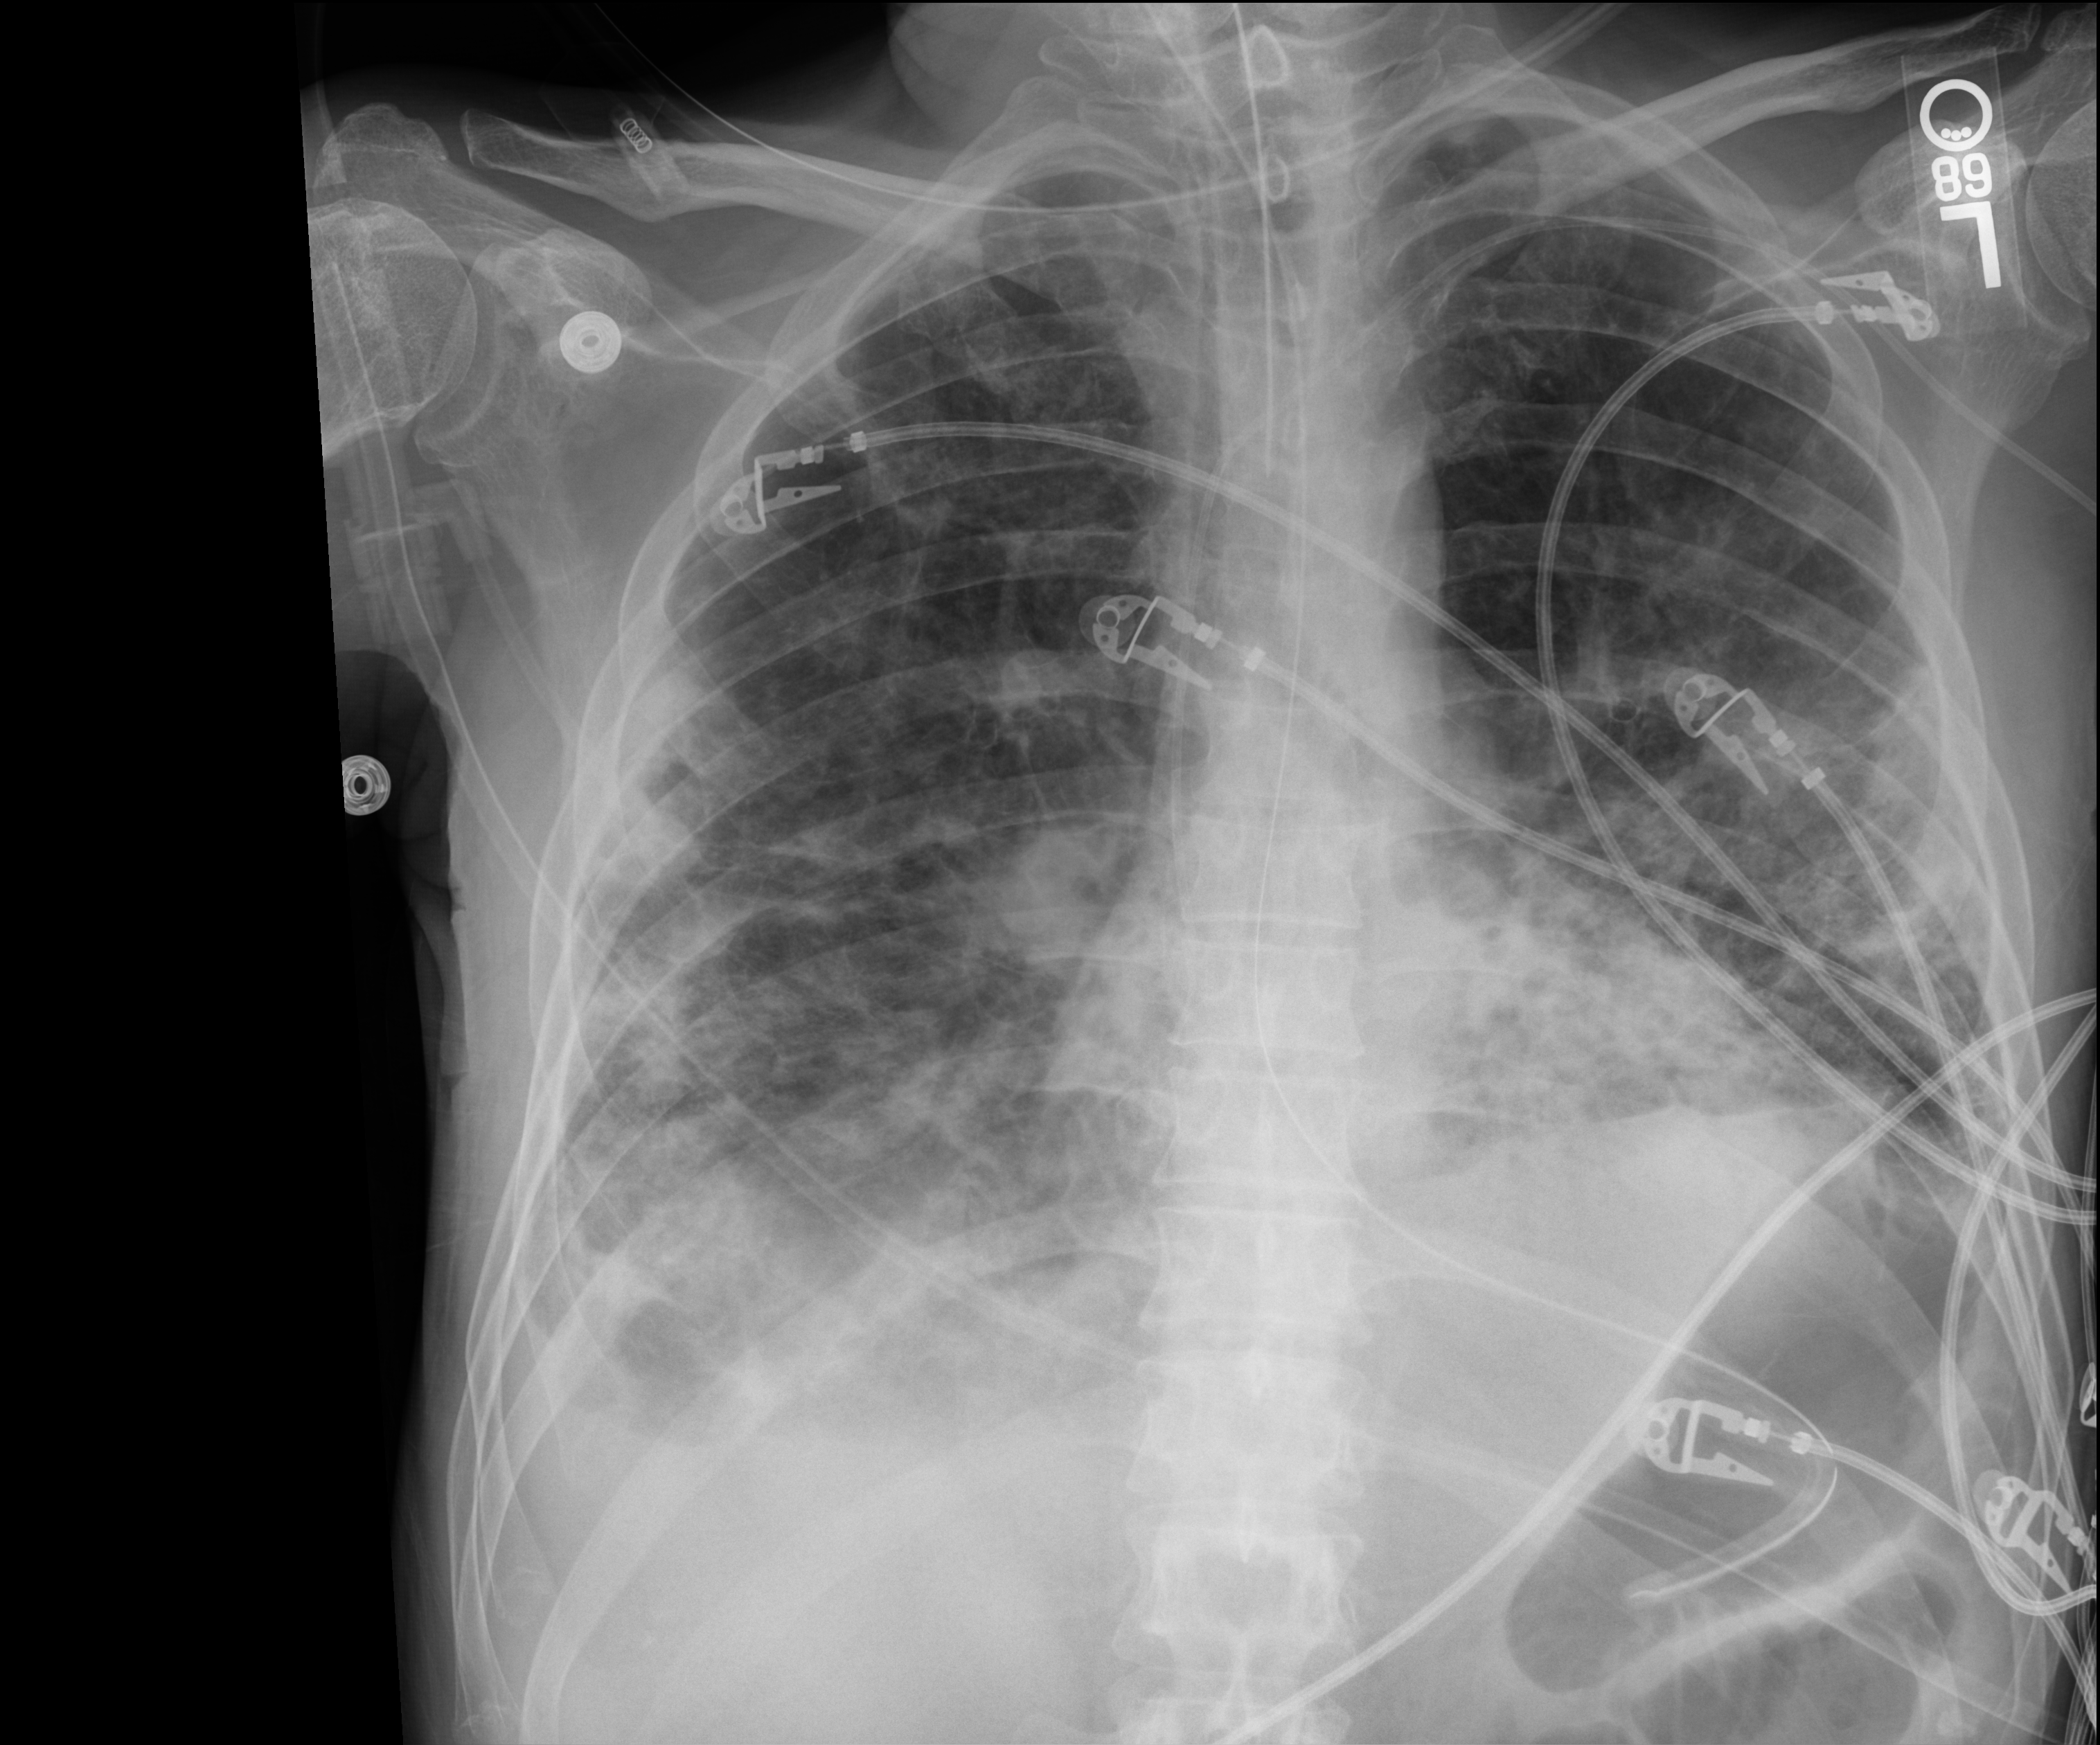
Chest X-ray; anteroposterior (AP) projection. Patient hospitalised with COVID-19; male, aged 18–59 years.
From the hospital-stay record, not from the radiograph (when in the stay this image was taken is not recorded):
- admitted to intensive care during this hospital stay: yes
- COPD (admission record): no